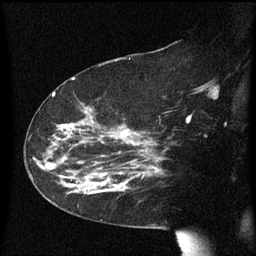
Breast MRI (dynamic contrast-enhanced), one sagittal slice. Dynamic contrast-enhanced series, image 2 of 3 at this slice position (ordered by acquisition). 1.5 T. TE 4.2 ms, TR 8.4 ms. 256 × 256 image matrix, field of view 200 × 200 mm. Female patient, age 63 years. Case-level facts recorded for this patient, not image findings: setting: breast cancer imaged before/during neoadjuvant chemotherapy; receptor status: HER2-positive.
Annotated regions visible in this slice (semi-automatically segmented with operator editing):
- analysis volume of interest (the breast-tissue region the enhancement analysis was run in; not a lesion): bounding box (x1, y1, x2, y2) in pixels: (71, 144, 147, 207)
- tumour enhancement mask (voxels above the 70 % enhancement threshold inside the analysis volume of interest): (102, 150, 144, 185)